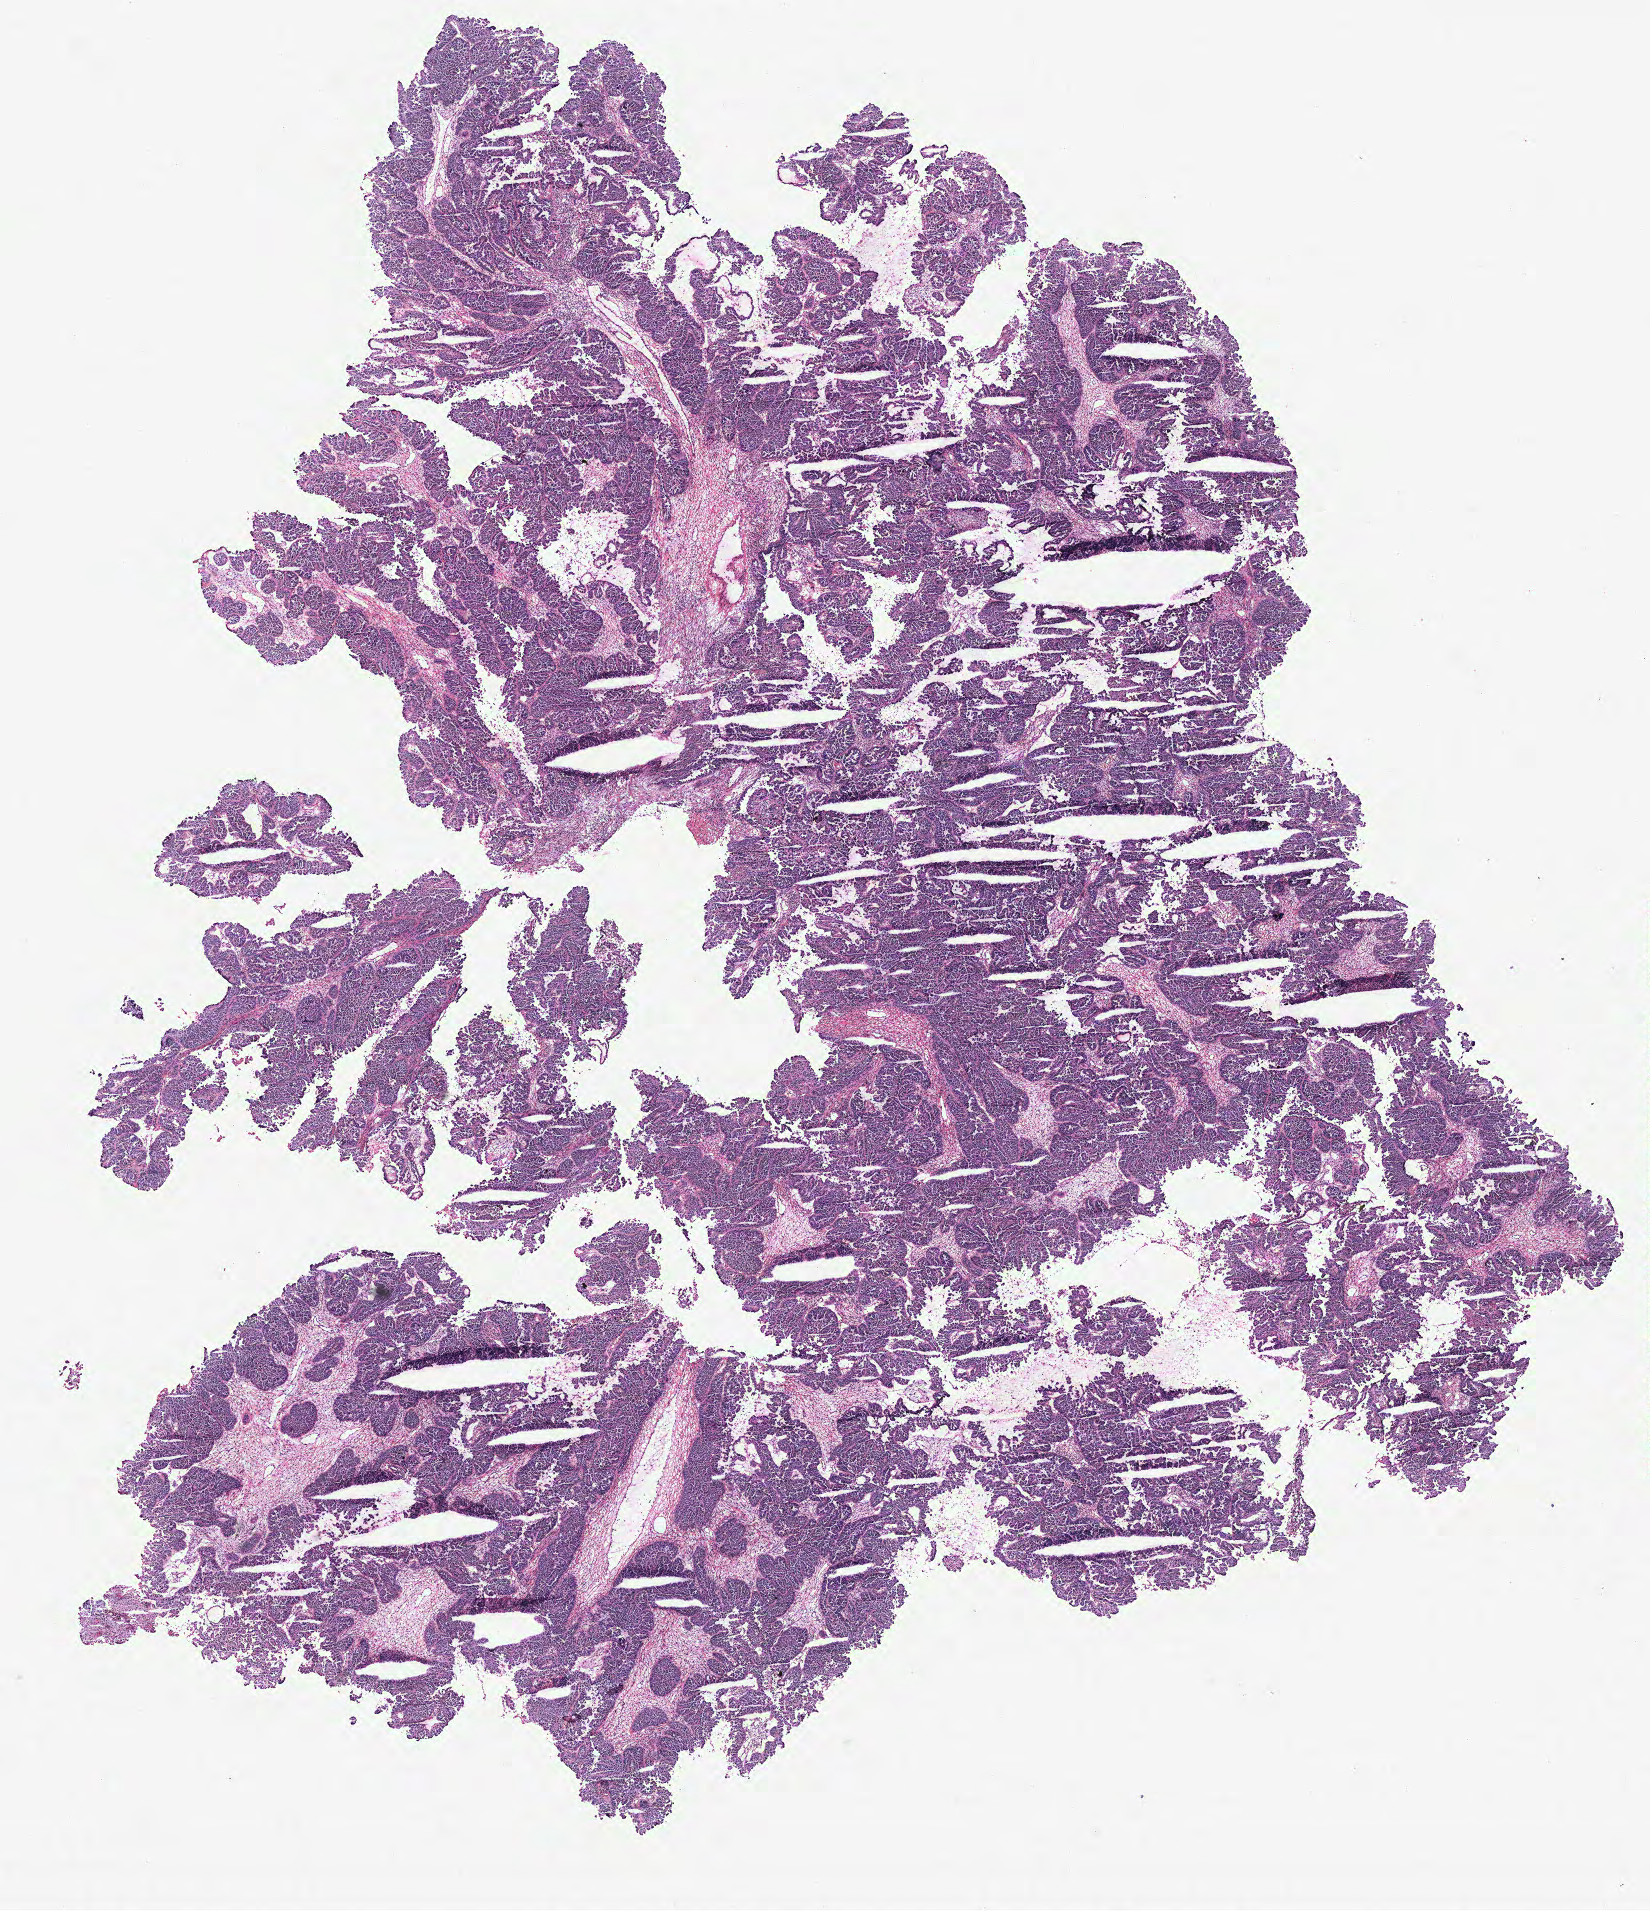
H&E-stained whole-slide image — low-resolution overview of the scanned area, about 13.2 x 15.3 mm (from a 40x scan). Tumour tissue sample, ovary. Patient: female, age 48 years.
Histologic diagnosis: Serous adenocarcinoma, NOS (fallopian tube). Primary tumour site (as recorded): fallopian tube.